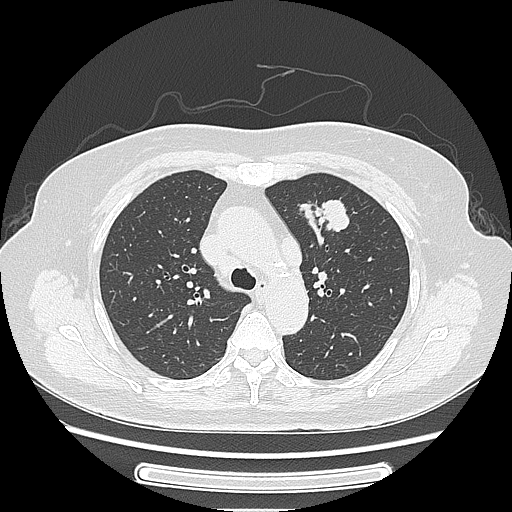
Chest CT, one axial slice. Position 169 of 227 along the scan axis. Reconstruction kernel LUNG. 120 kVp. Lung window (W 1500 / L -600 HU). 1.25 mm slice thickness. 512 × 512 image matrix, field of view 363 × 363 mm. Female patient, age 77 years. Case-level facts recorded for this patient, not image findings: clinical TNM (as recorded): T1c N3 M0; histopathological grade: G2-3.
Annotated regions visible in this slice (bounding box drawn by a radiologist):
- lung tumour (recorded histology: adenocarcinoma): bounding box [x1, y1, x2, y2] px = [299, 190, 360, 245]